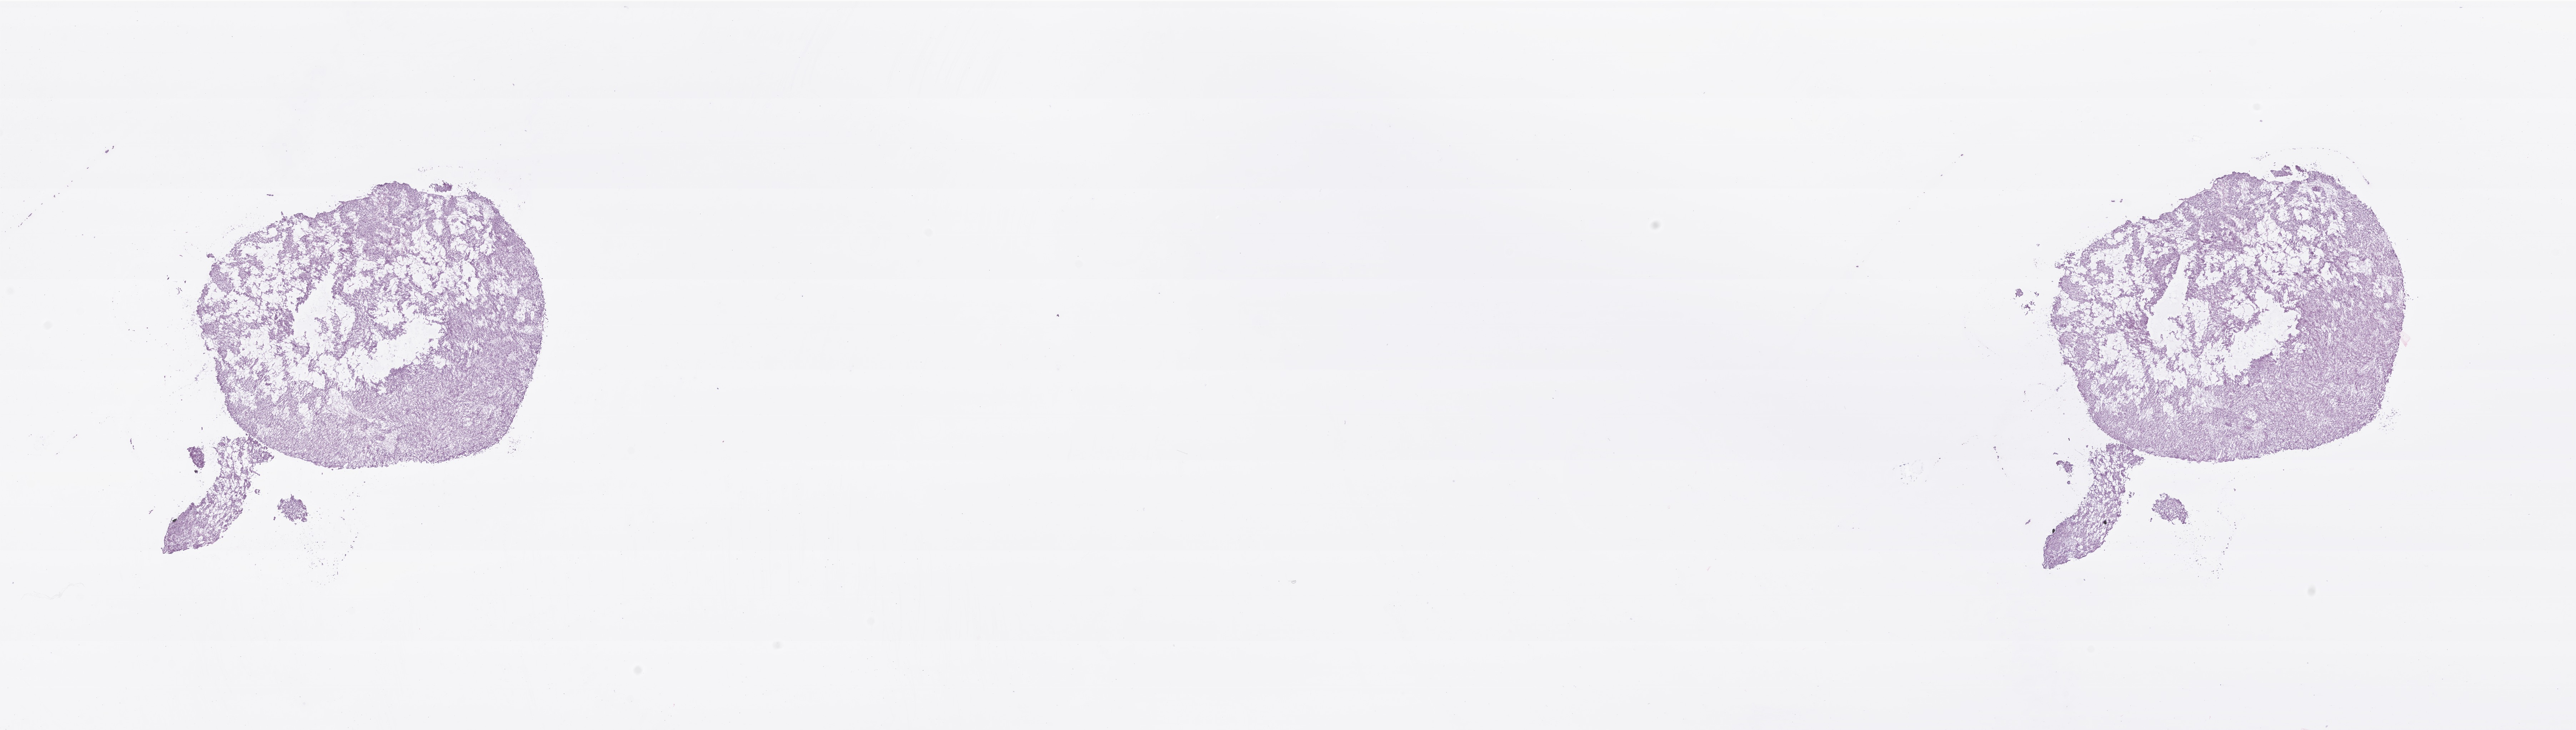
Digitized H&E-stained section of tumor tissue from the stomach, whole scanned area (about 30.3 x 8.6 mm) shown as a low-resolution overview. Frozen section. Patient: female, age 214 months (17 years 10 months).
* diagnosis: Gastrointestinal stromal tumor